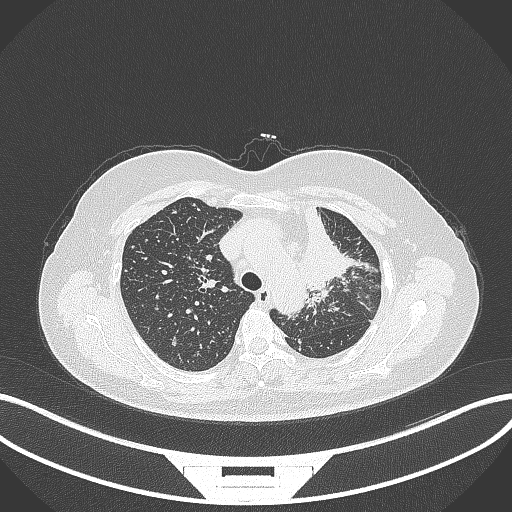
Chest CT, one axial slice. Slice 248 of 348 in the series (ordered by position). 120 kVp. Lung window (W 1500 / L -600 HU). 1 mm slice thickness. 512 × 512 image matrix, field of view 400 × 400 mm. Patient: female, 49 years. From the clinical record (not read from this slice): clinical TNM (as recorded): T1c N0 M1.
Annotated regions visible in this slice (bounding box drawn by a radiologist):
- lung tumour (recorded histology: adenocarcinoma): bounding box [x1, y1, x2, y2] px = [287, 203, 360, 293]